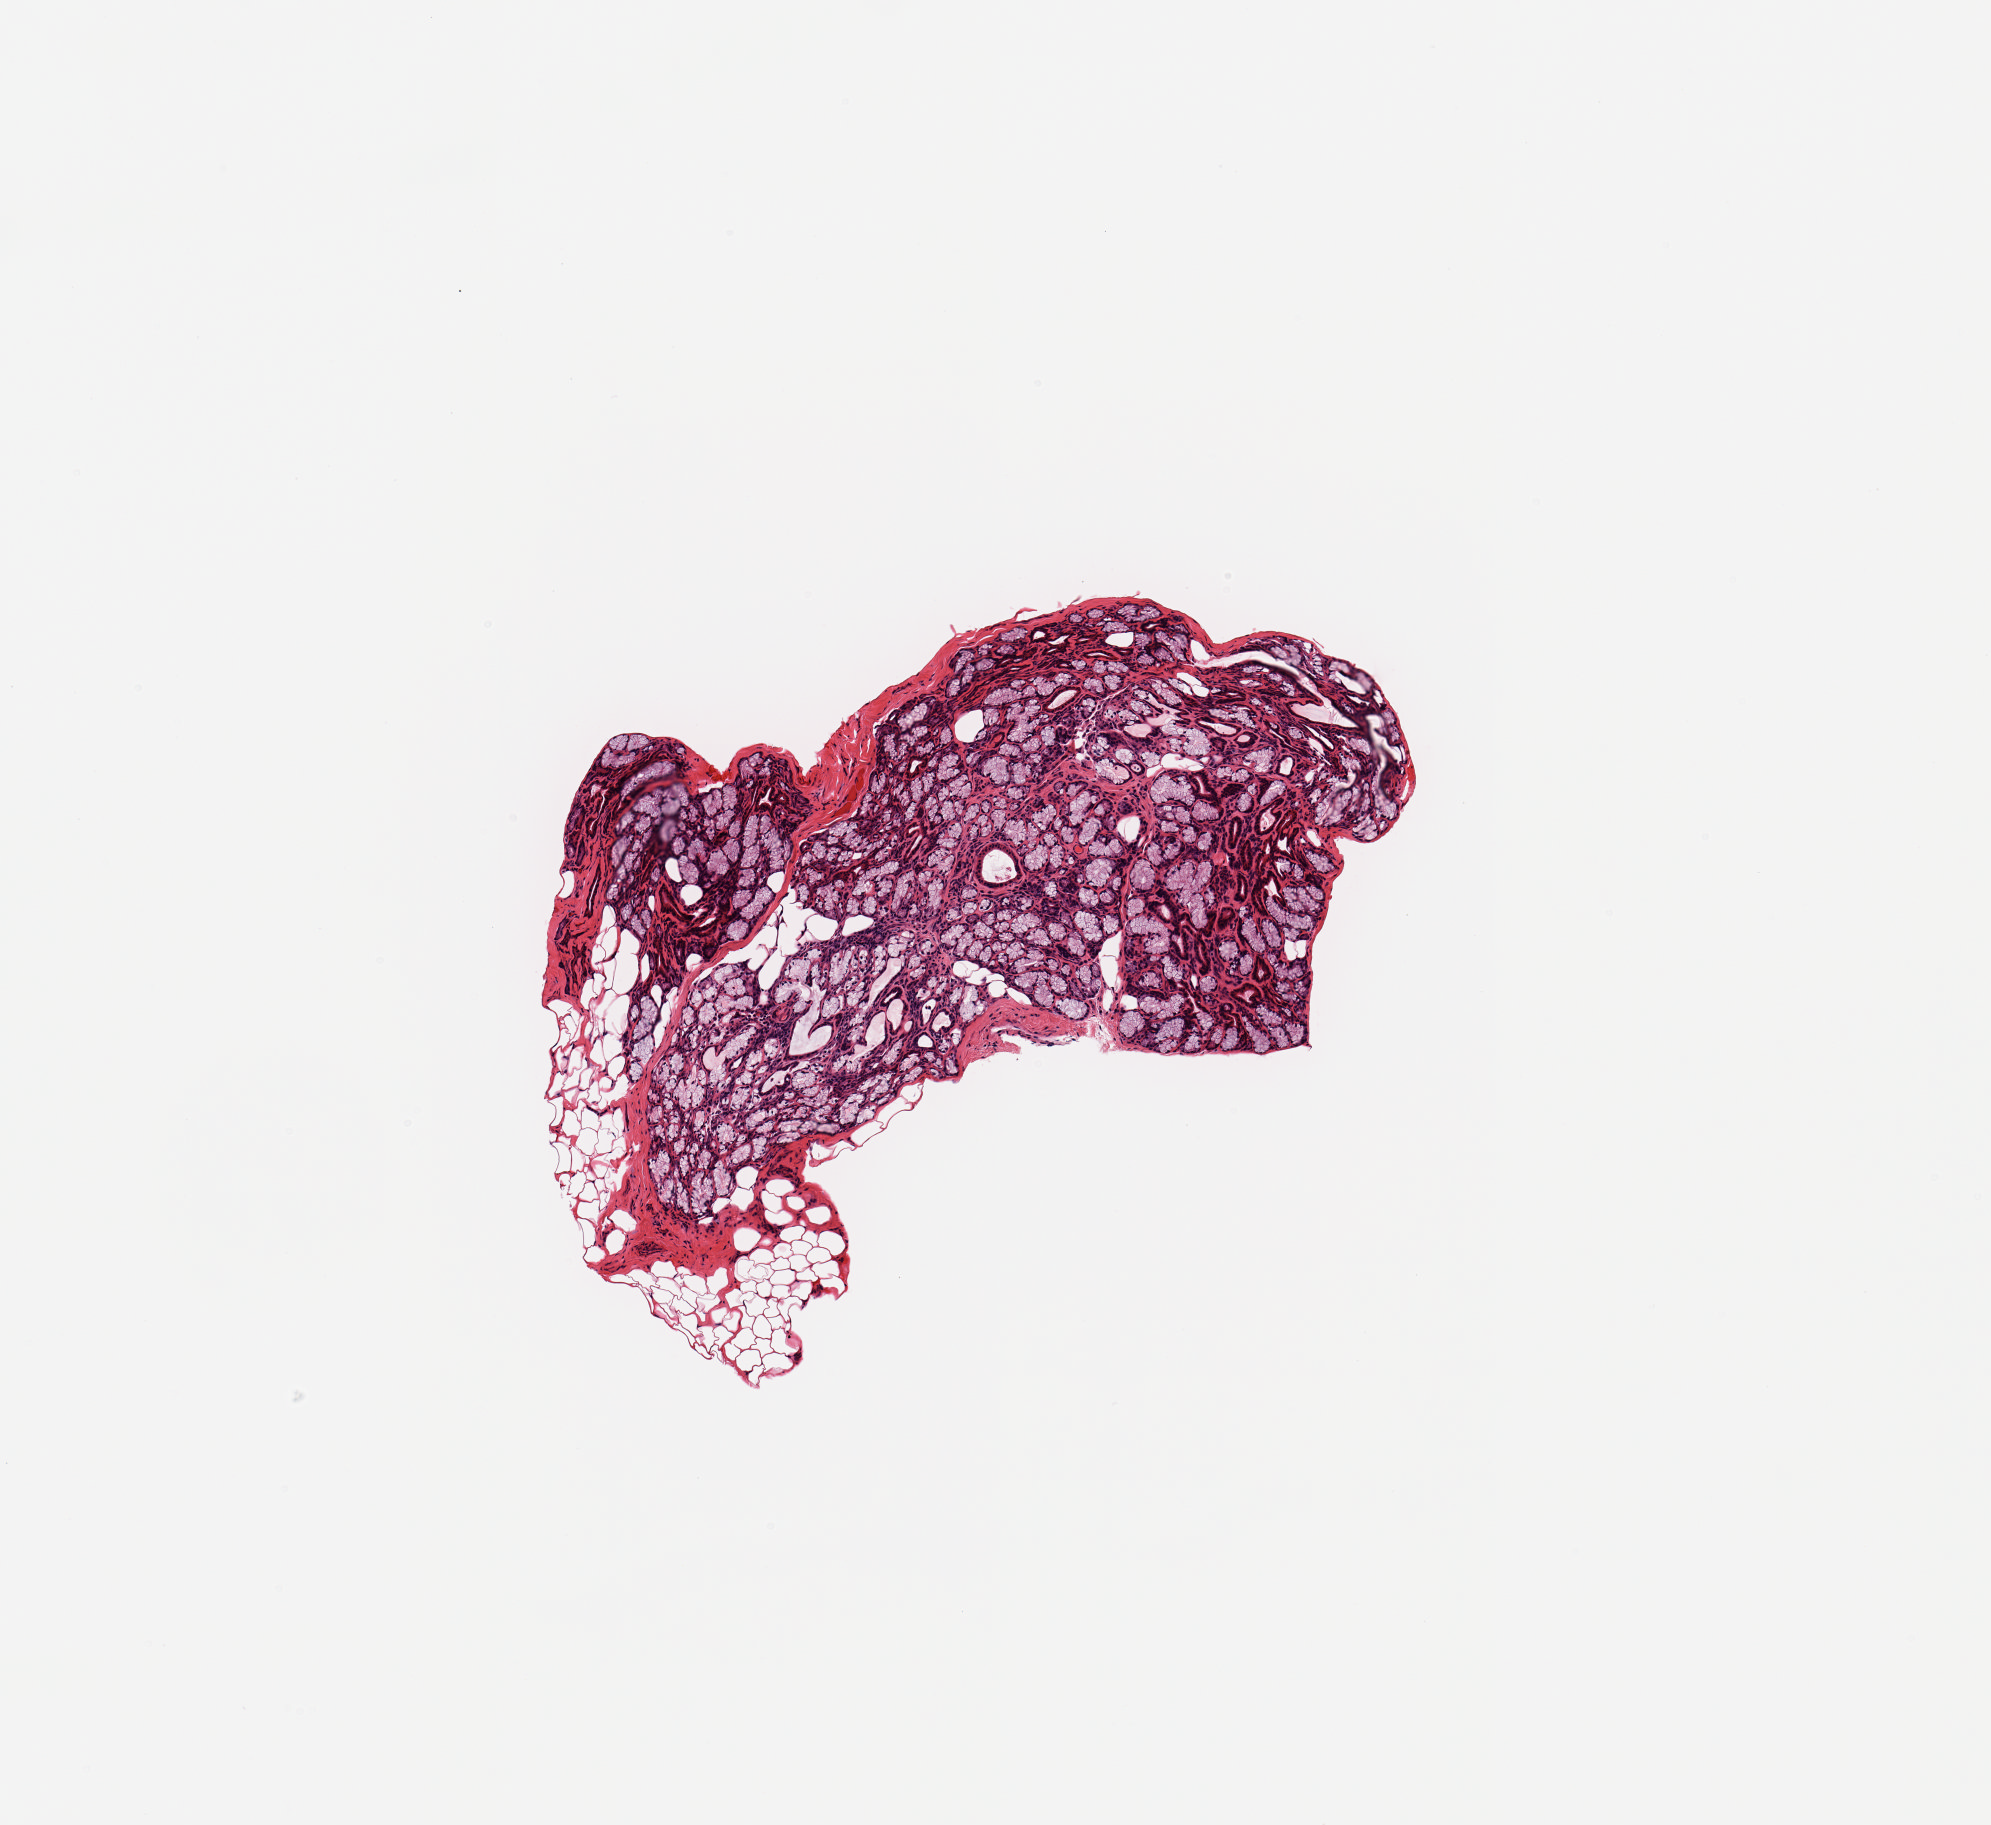
Digitized haematoxylin and eosin-stained section — low-resolution overview of the scanned area, about 3.9 x 3.6 mm (slide scanned at 20x); PAXgene-fixed paraffin-embedded (PFPE) section; sampled site (target tissue): minor salivary gland; tissue donor sample. Female donor.
Pathologist's review note for this sample: 1 piece glandular element is ~90% tissue; adherent nubbin of fat is remainder.